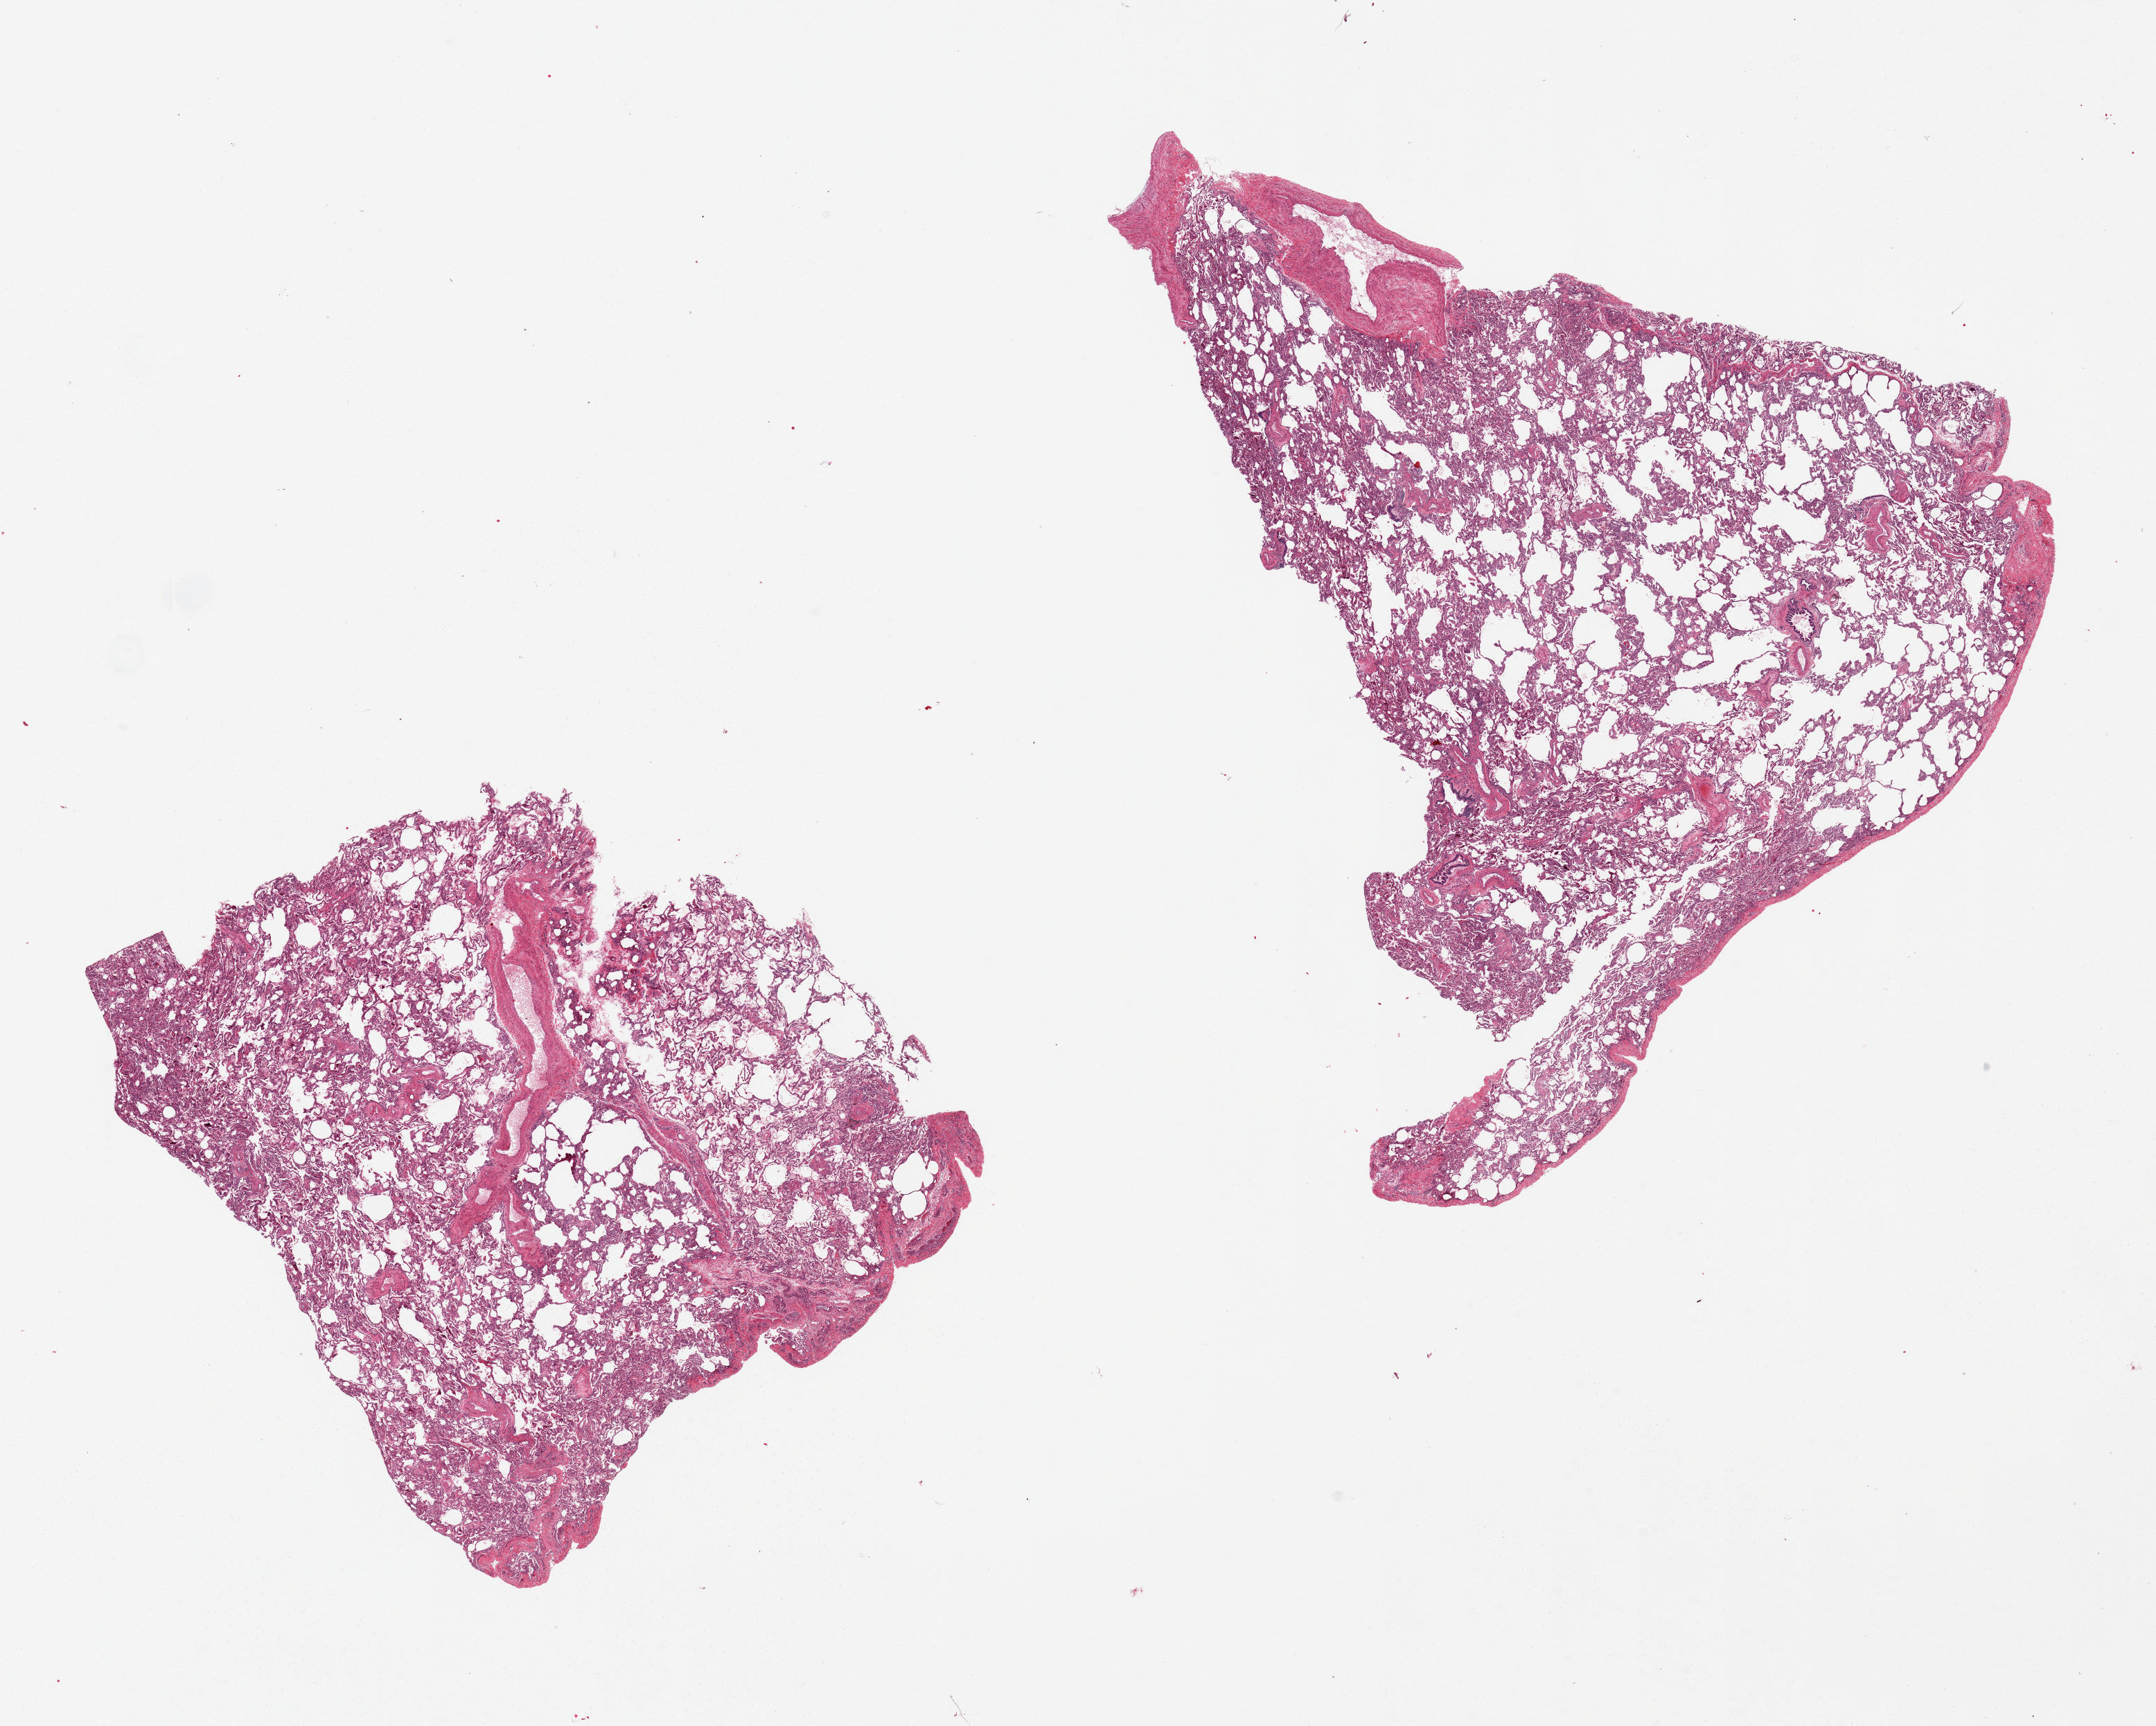
Digitized haematoxylin and eosin-stained section, shown as a low-resolution overview of the whole scanned area (about 24.6 x 19.7 mm, slide scanned at 20x); PAXgene-fixed, paraffin-embedded tissue; sampled site (target tissue): lung; tissue donor sample.
• pathologist's review note for this sample: 2 pieces; some emphysematous change and atelectasis